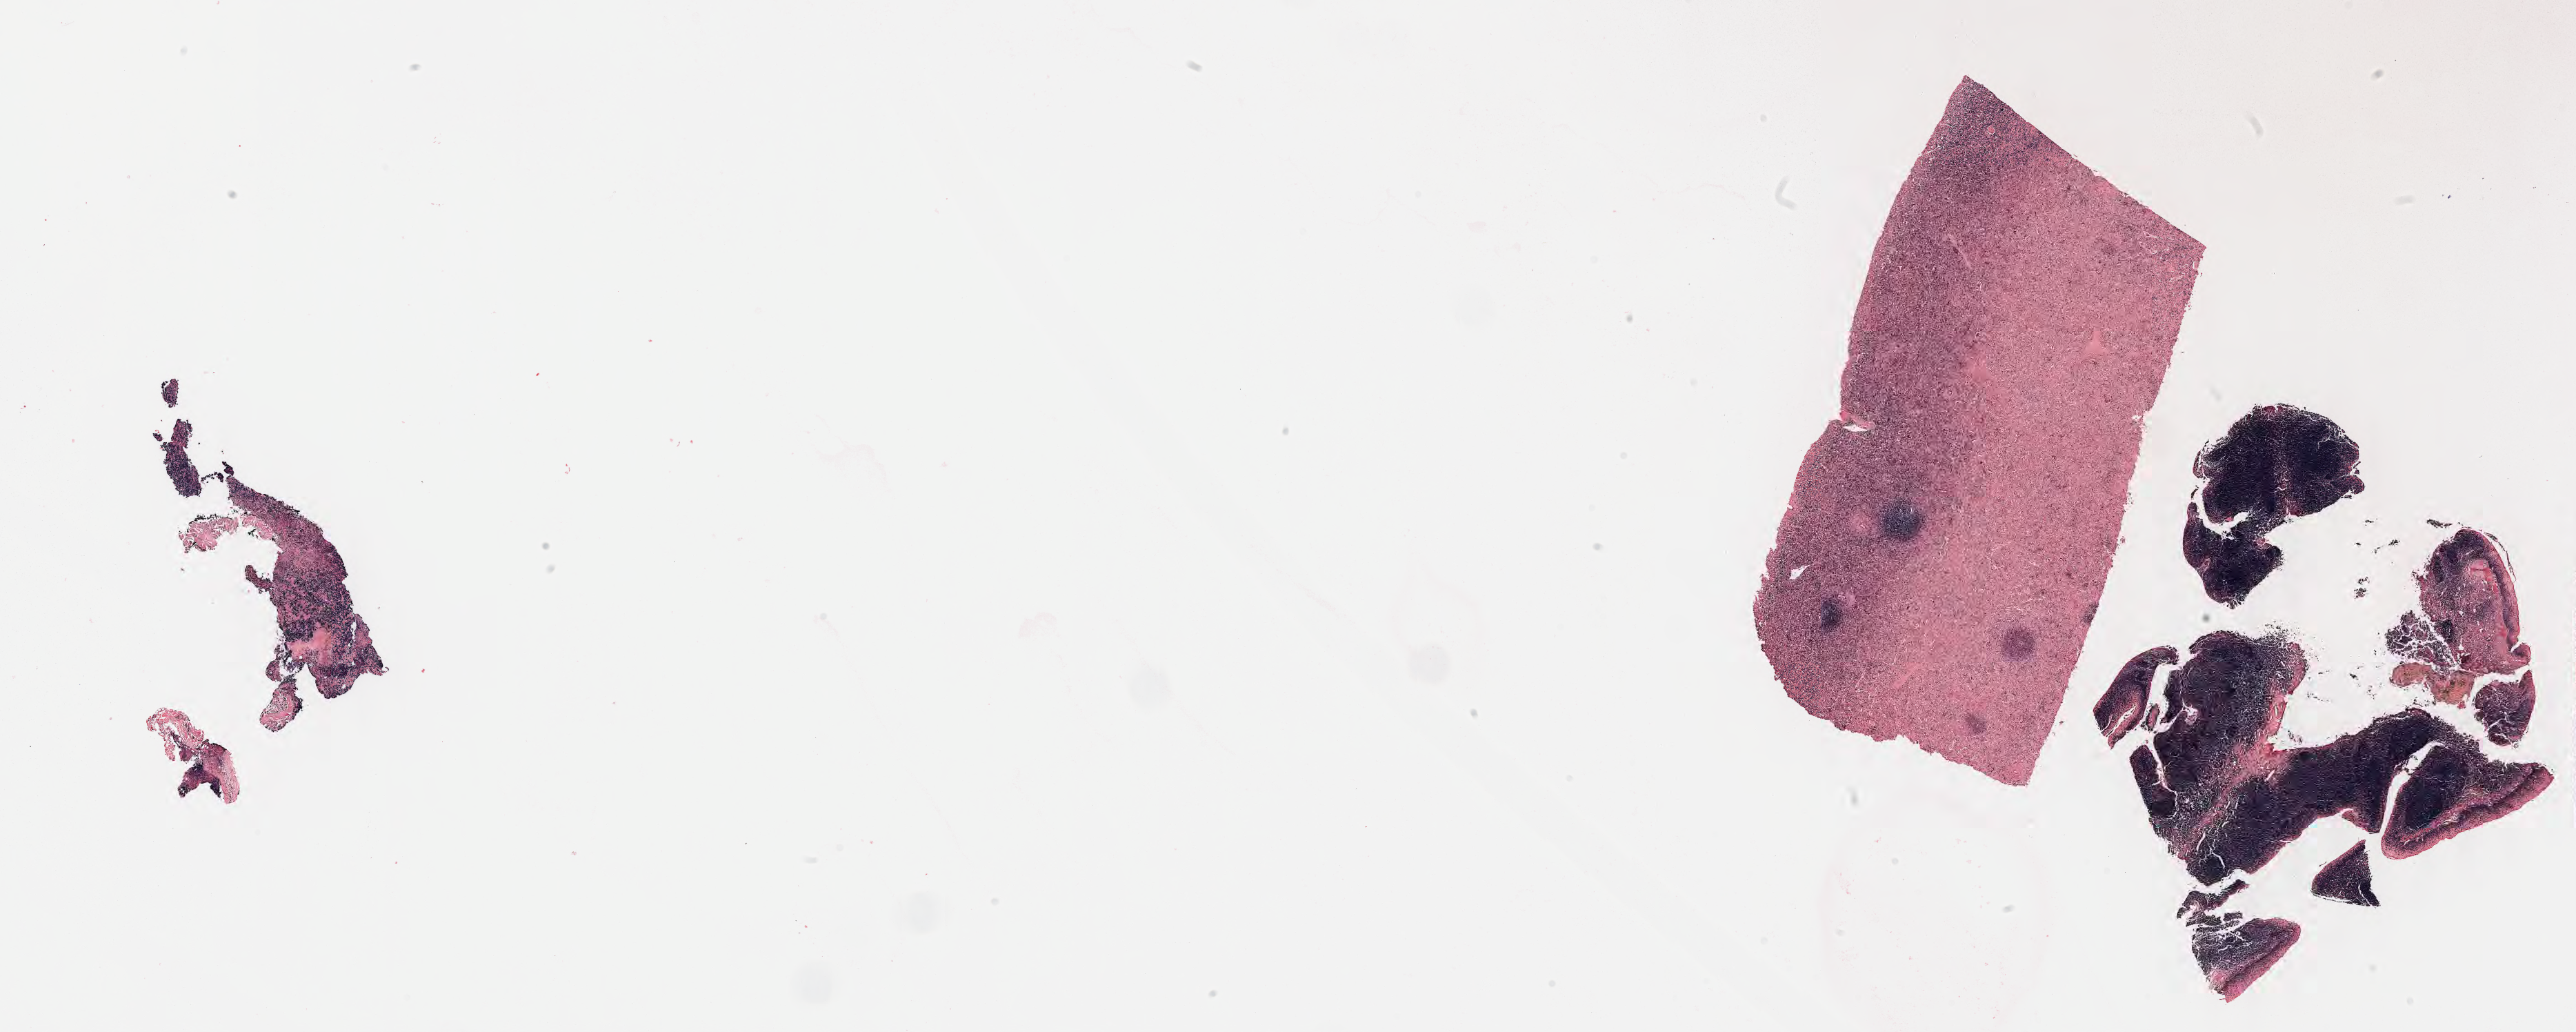
Whole-slide image; stain recorded as Iodonitrotetrazolium, whole scanned area (about 30.2 x 12.1 mm) shown as a low-resolution overview. Specimen: tumor tissue. Patient female; 27 years old.
Diagnosis: Diffuse large B-cell lymphoma, NOS.